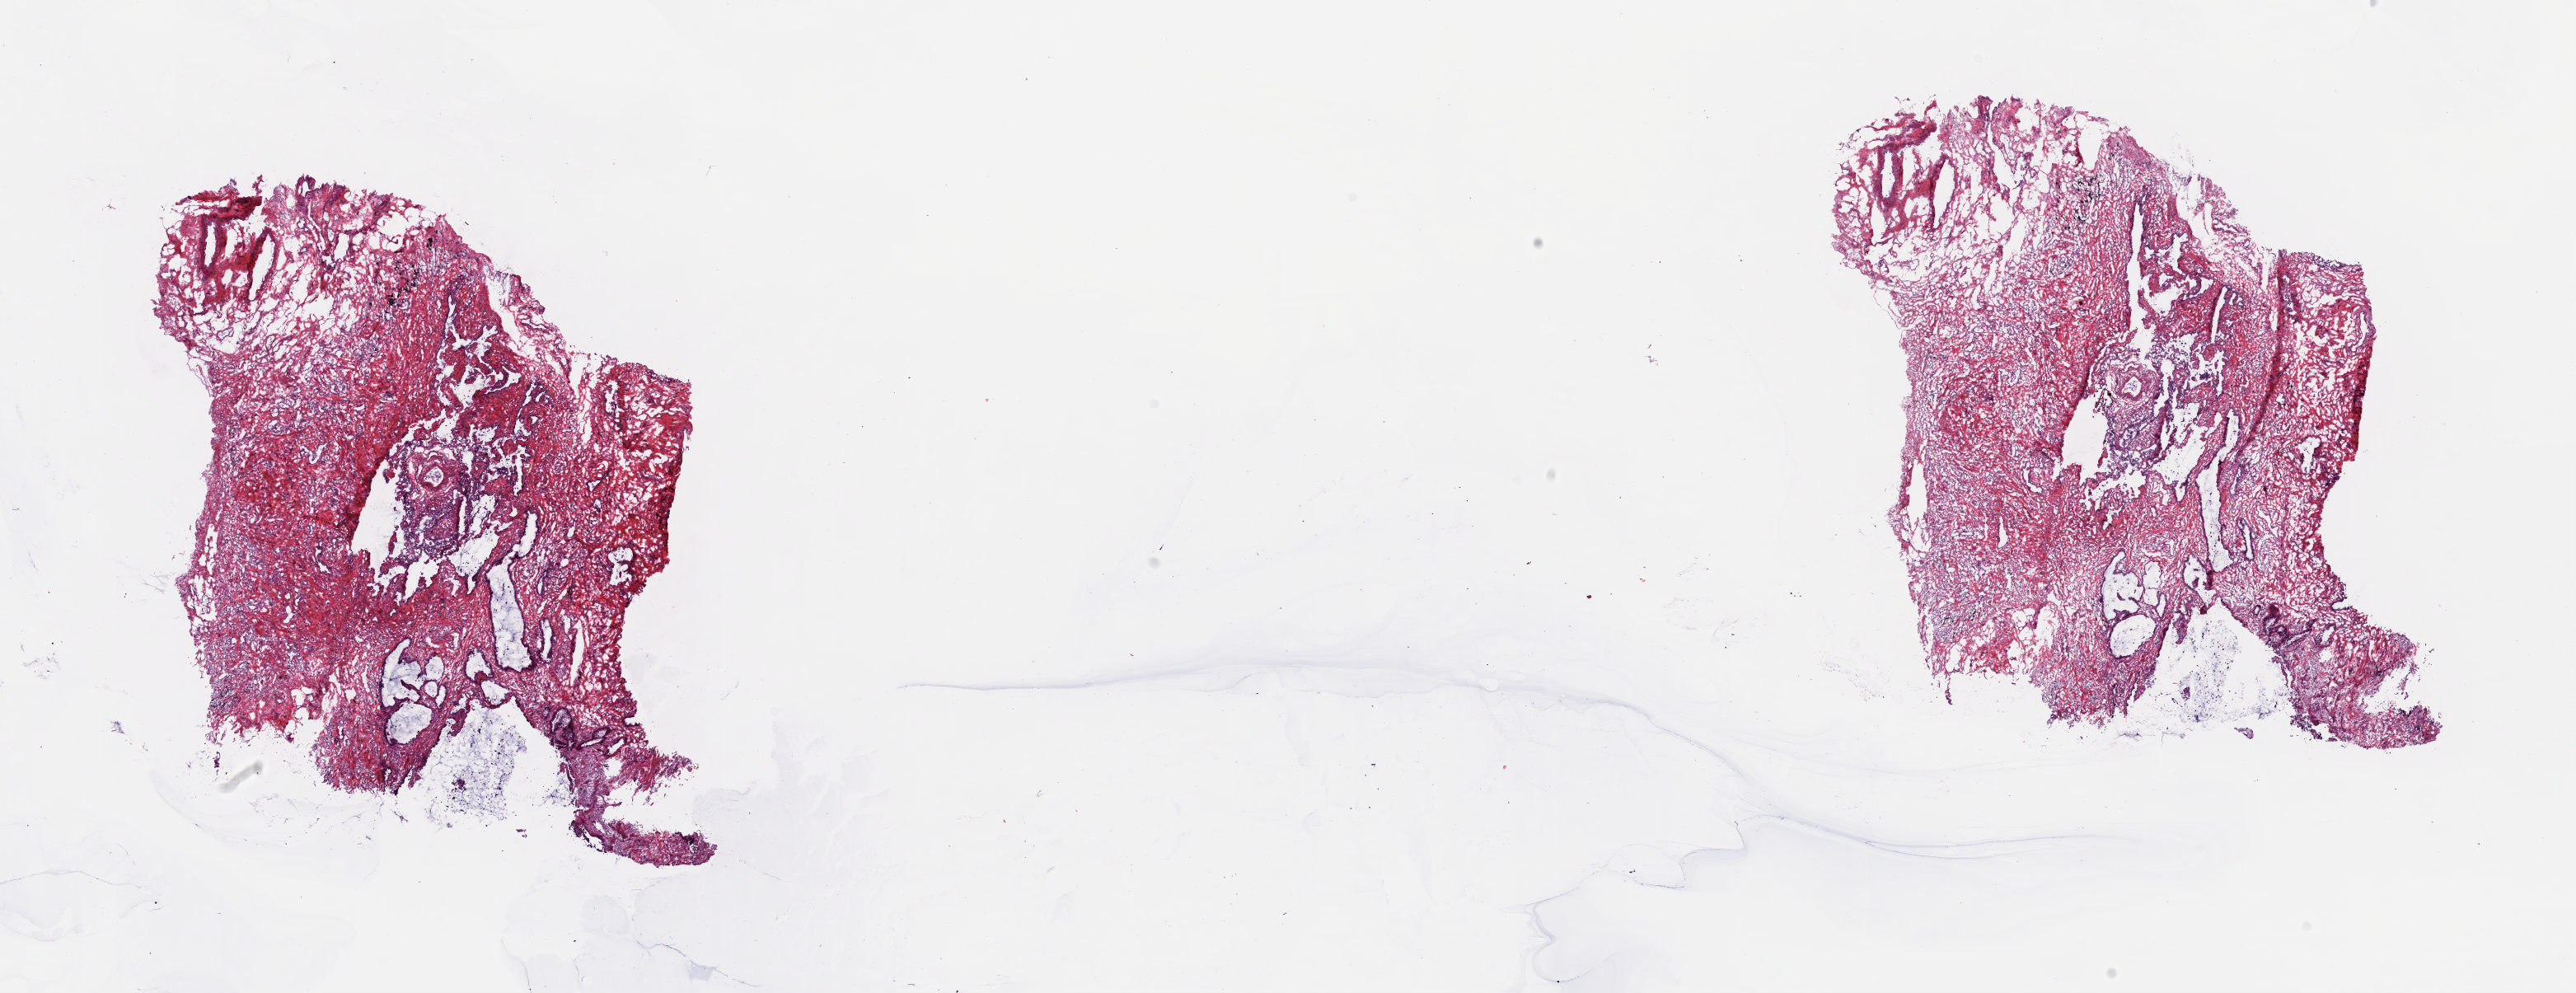
Whole-slide histology image, H&E-stained — a low-resolution overview of the entire scanned area, about 24.8 x 9.6 mm (from a 20x scan), frozen section from the top of the tissue portion, sample: solid tissue normal (non-tumour tissue), lung. Patient sex: male. Slide review estimates, as recorded: tumour cells 0%, tumour nuclei 0%, normal cells 20%, stromal cells 80%, necrosis 0%. Infiltration values recorded for this section: lymphocyte infiltration 5%, monocyte infiltration 5%, neutrophil infiltration 2%.
This section: solid tissue normal (non-tumour) sample from the same patient. Patient diagnosis: Squamous cell carcinoma, NOS.